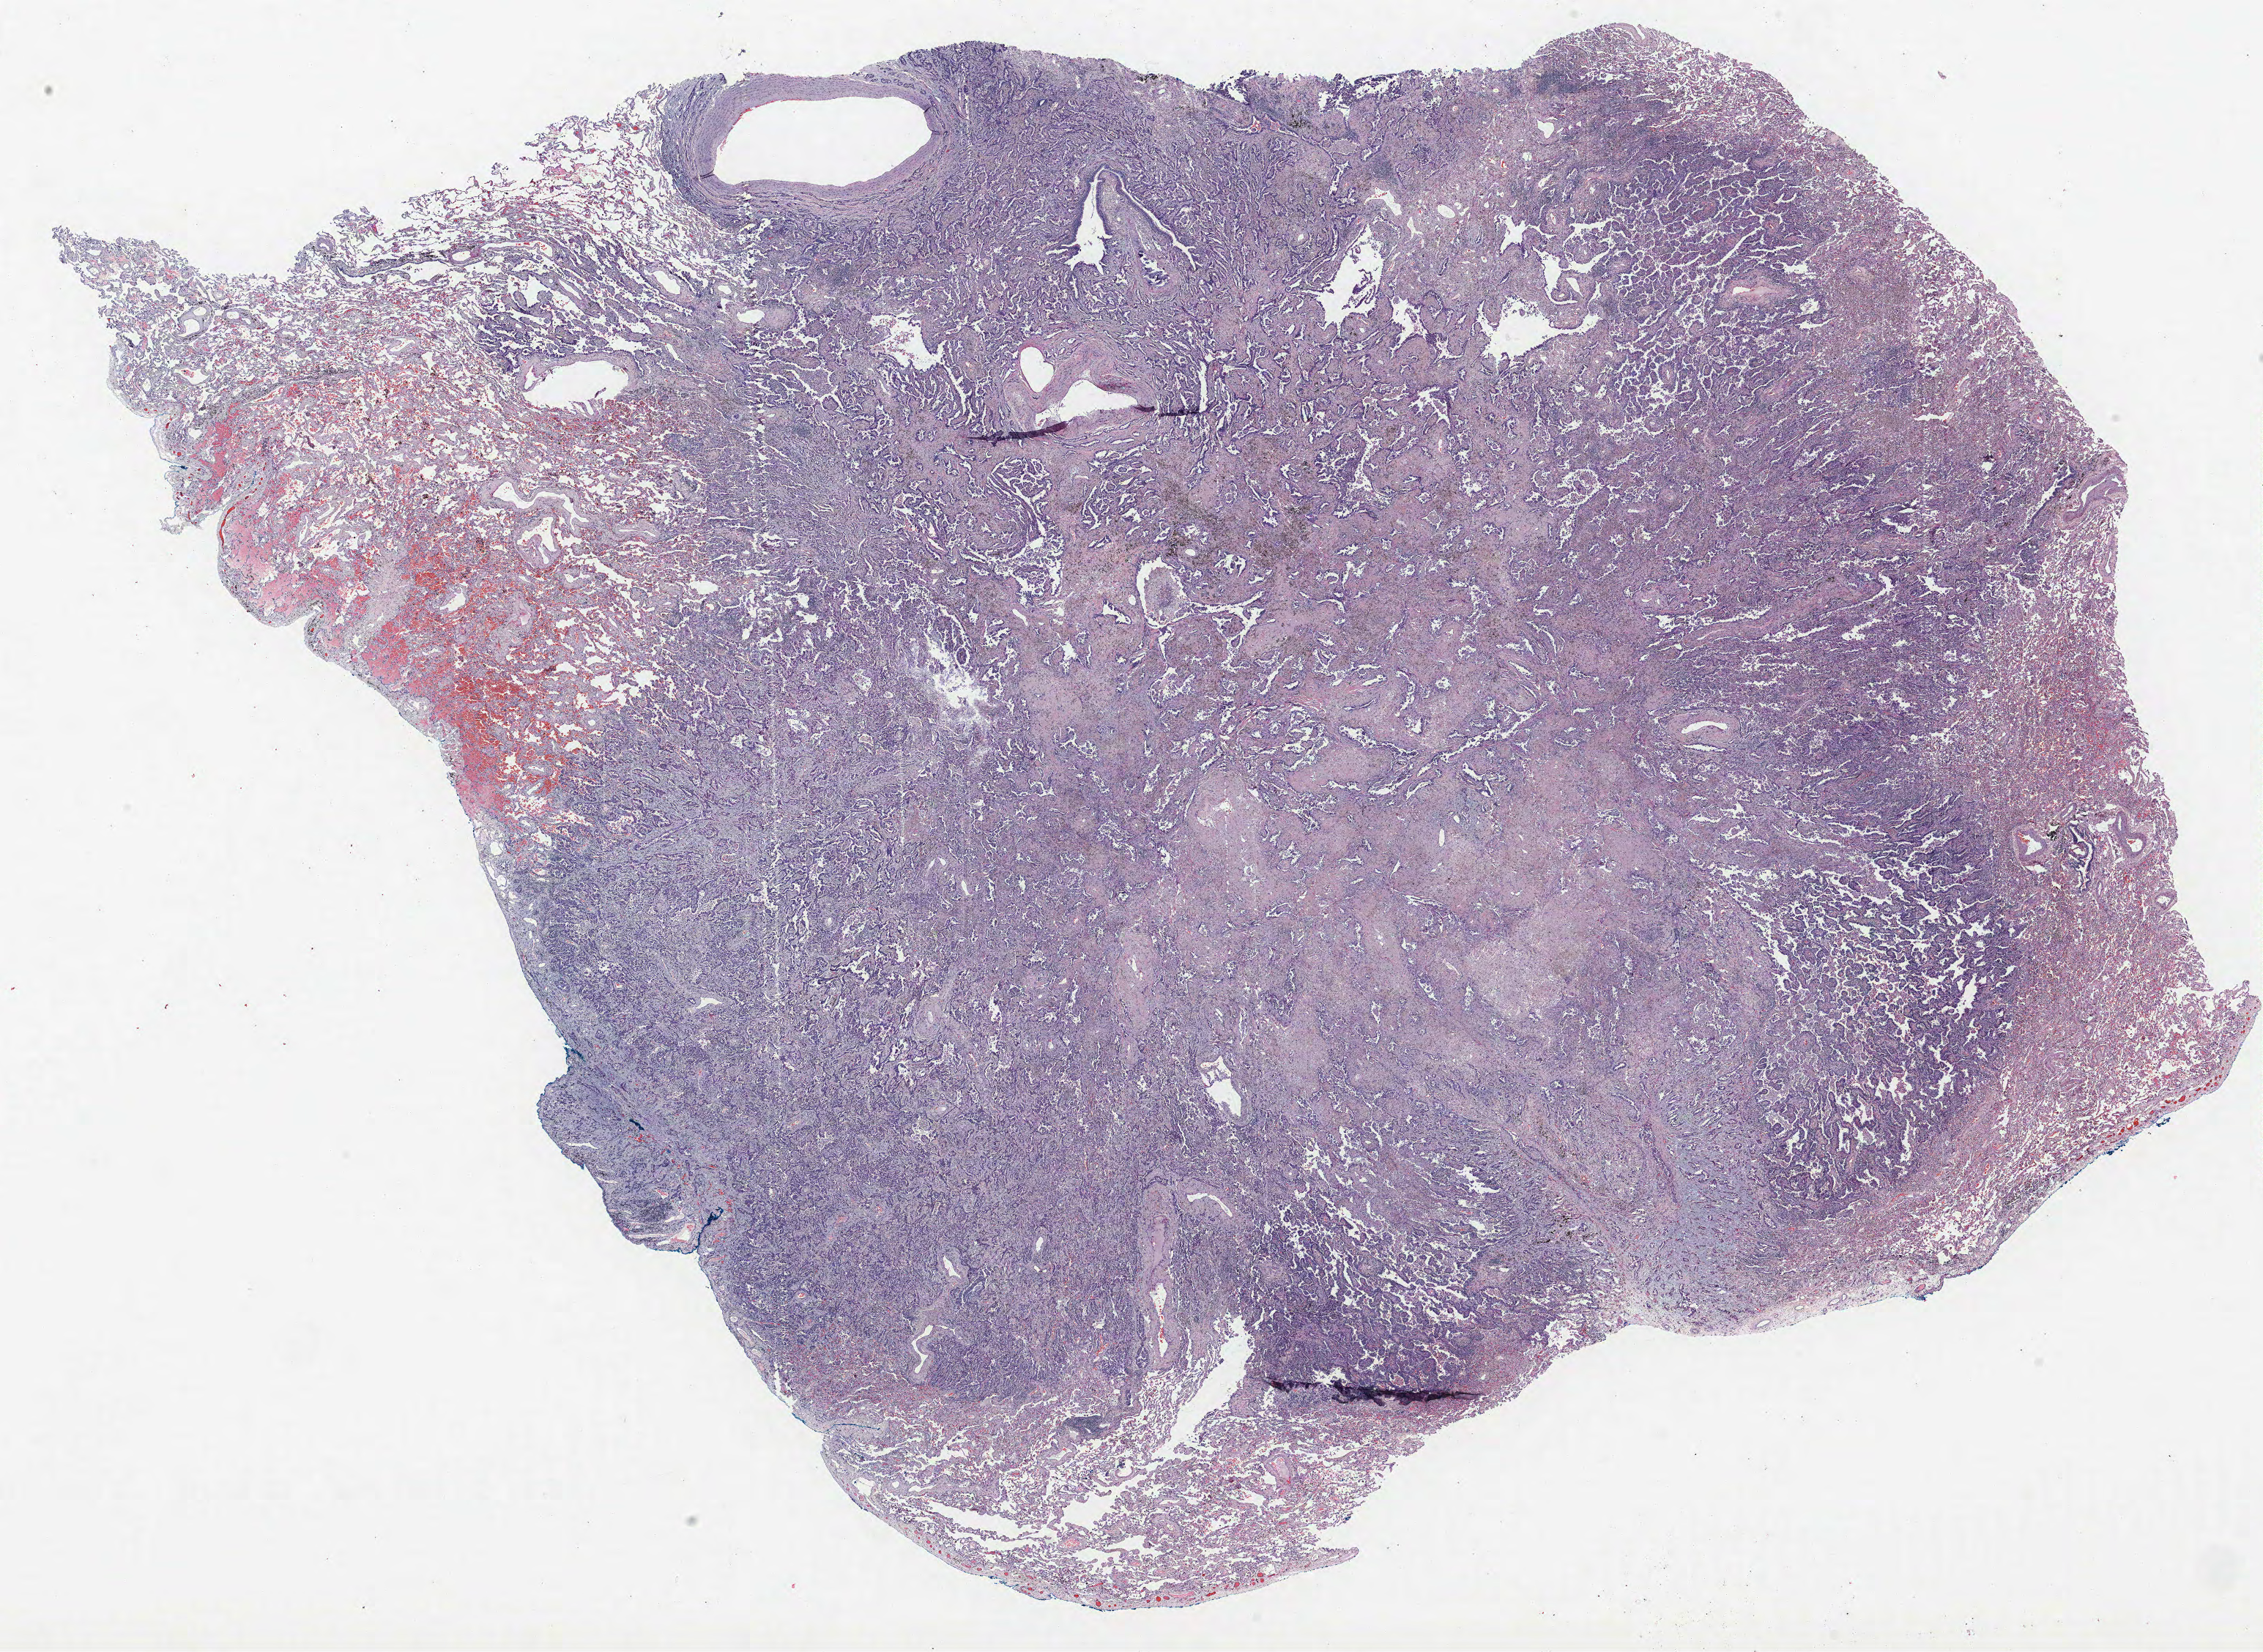
Hematoxylin and eosin (H&E) stained whole-slide image — whole scanned area (about 24.7 x 18.1 mm) shown as a low-resolution overview, formalin-fixed paraffin-embedded (FFPE) section, lung. Female patient, aged 56 at enrolment. Current smoker at enrolment. Grade: well differentiated (G1).
Tumour size (pathology): 20 mm. Stage (AJCC 6th edition): IA. Primary tumour location (clinical record): left lower lobe. Participant's lung-cancer diagnosis: Bronchiolo-alveolar adenocarcinoma, NOS. ICD-O-3 topography: lower lobe of lung (C34.3).